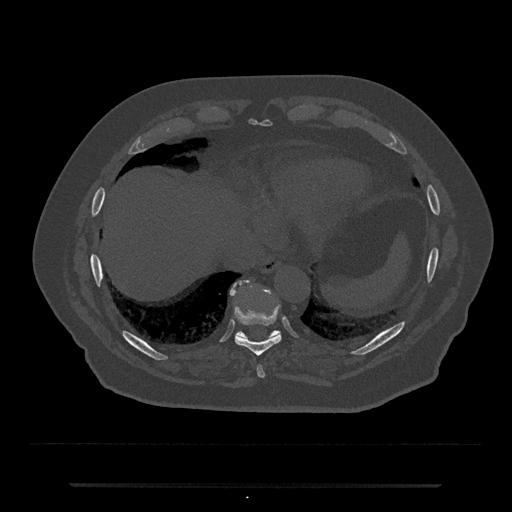
CT including the spine, one axial slice; slice 745 of 797 in the series (ordered by position); bone window (W 1800 / L 400 HU); 0.5 mm slice thickness; 512 × 512 image matrix, field of view 434 × 434 mm. Patient: male, 80 years. Case-level facts recorded for this patient, not image findings: primary cancer: prostate; vertebrae with lytic lesions (as recorded): L1, T11.
Annotated regions visible in this slice (semi-automatic segmentation, software-assisted and operator-edited):
- T10 vertebra: box from (x=230, y=281) to (x=281, y=339) px
- T8 vertebra: (x=257, y=366)–(x=265, y=378)
- T9 vertebra: (x=235, y=308)–(x=281, y=356)